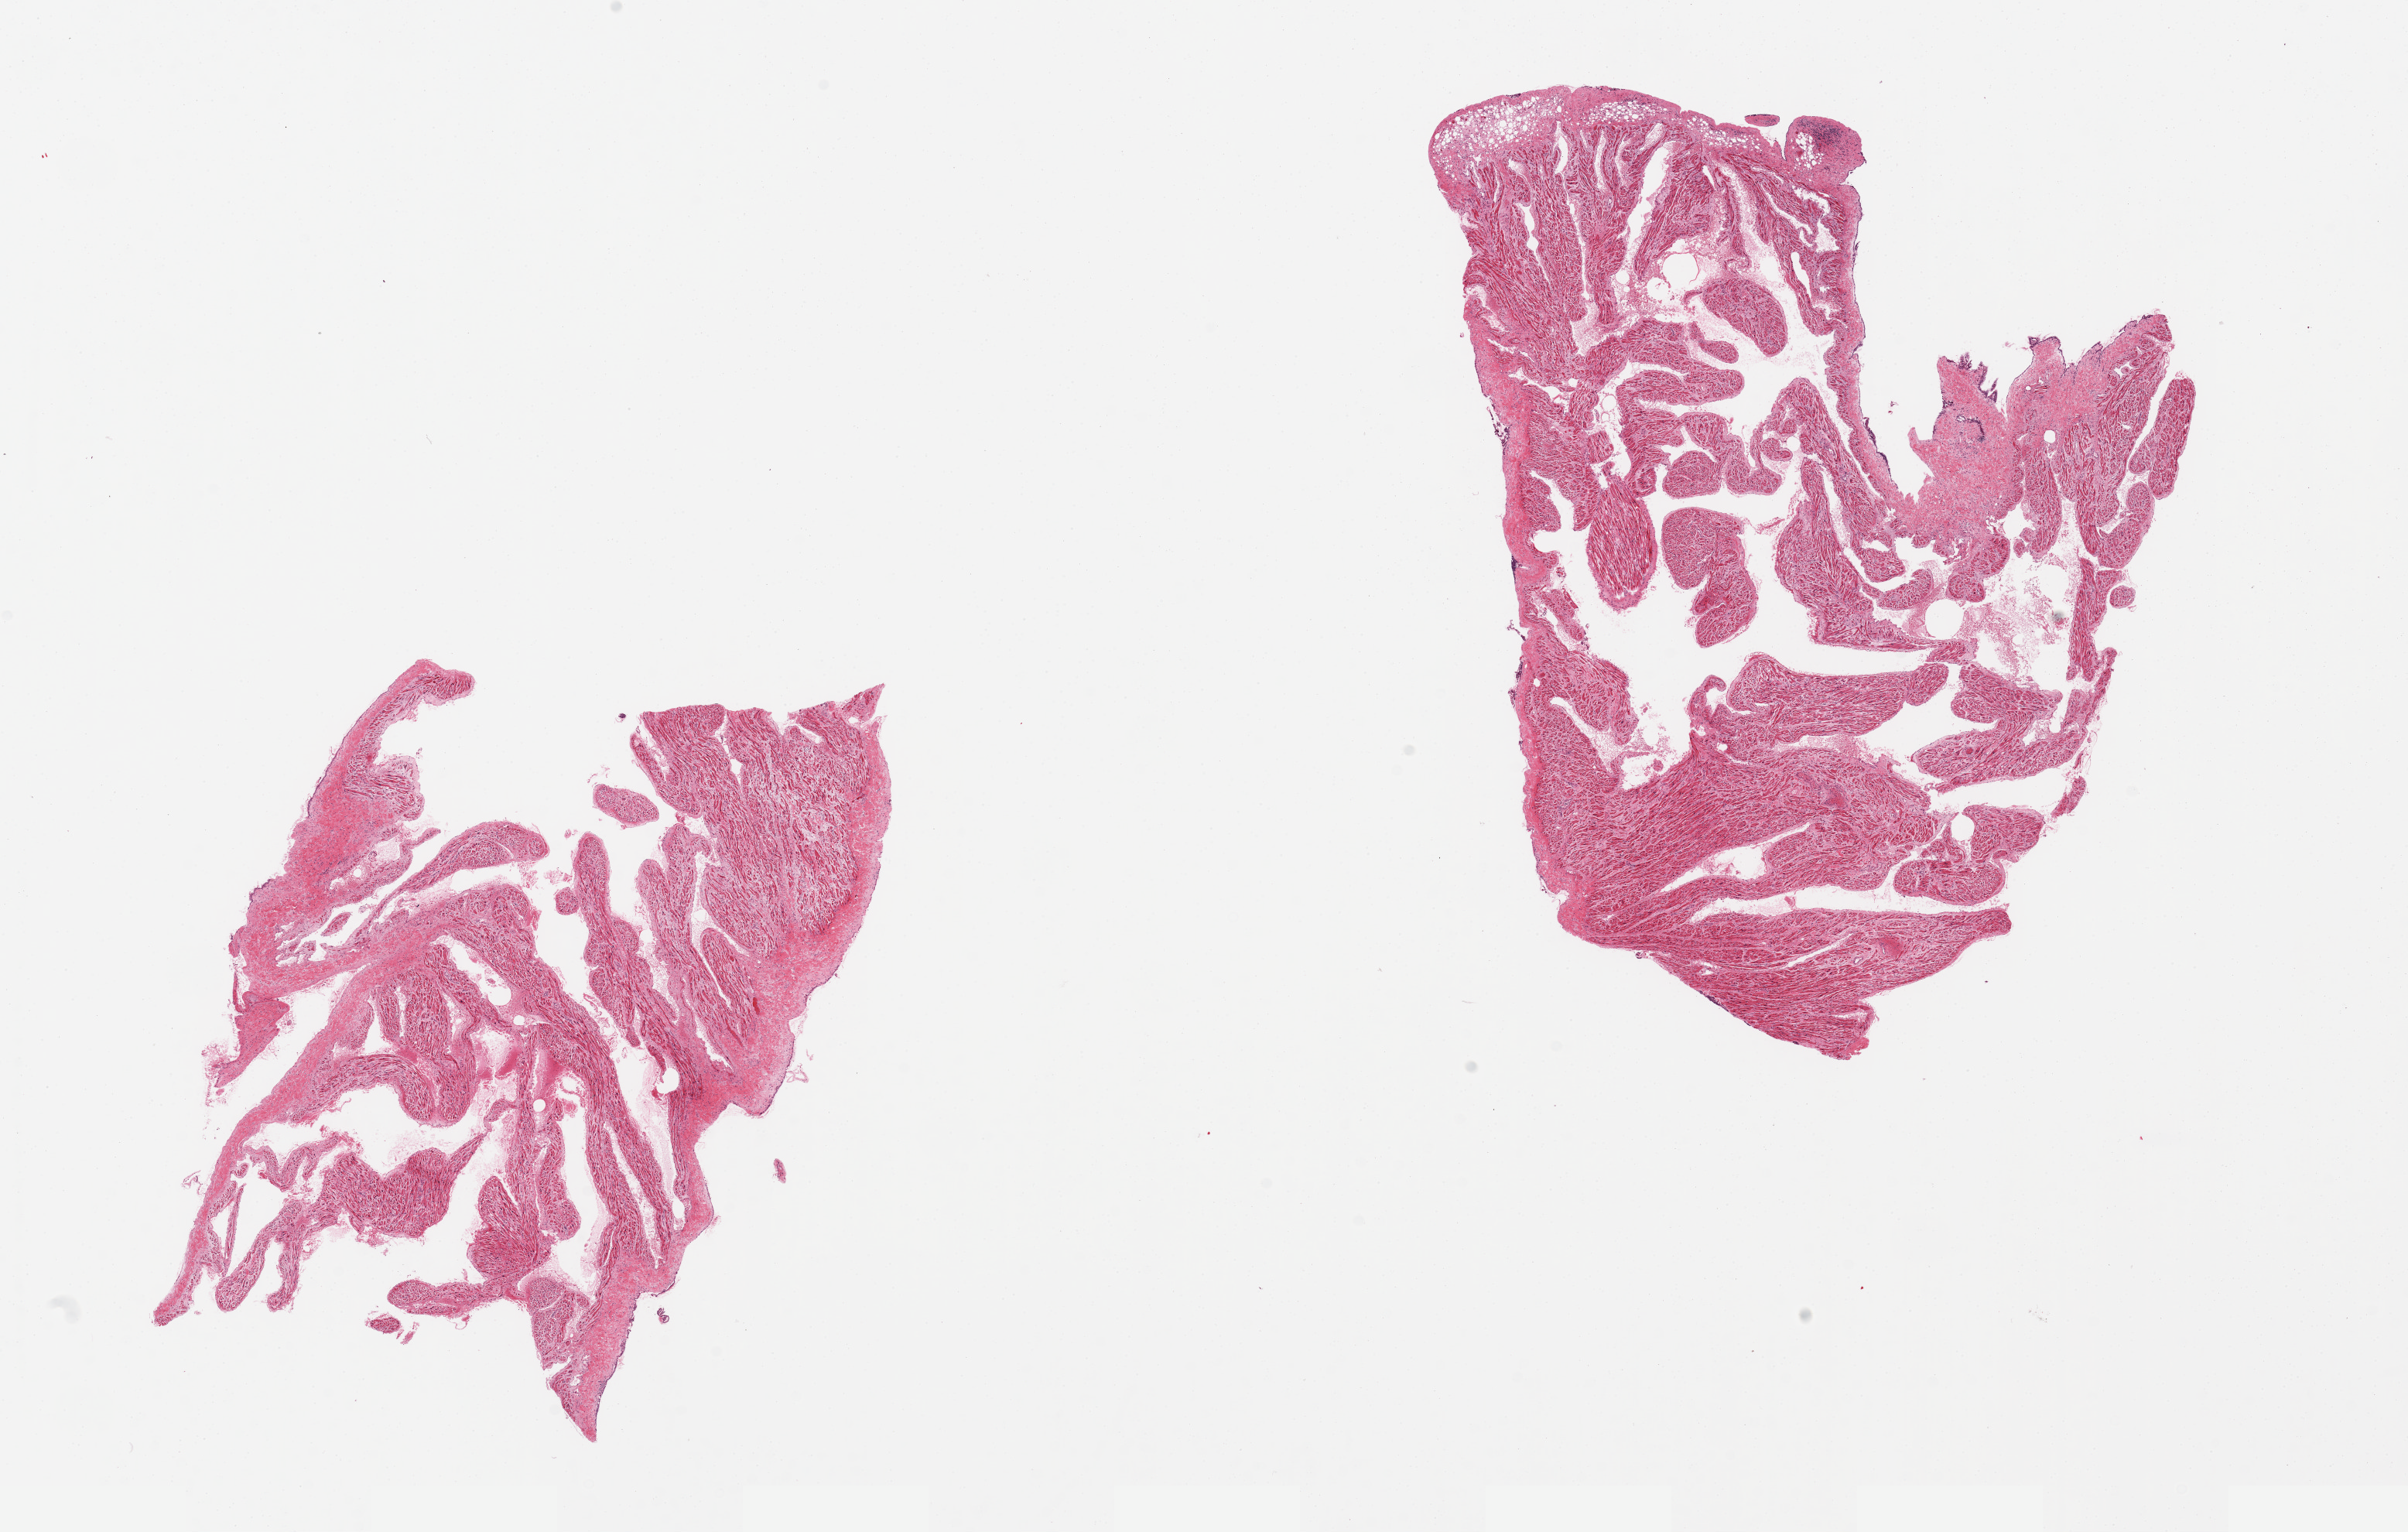
Digitized hematoxylin and eosin (H&E)-stained section, a low-resolution overview of the entire scanned area, about 24.6 x 15.7 mm, PAXgene-fixed paraffin-embedded (PFPE) section, sampled site (target tissue): auricular appendage, tissue donor sample.
Review note (as recorded): 2 pieces, no abnormalities.